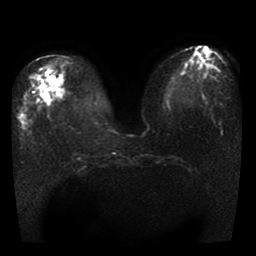
Breast MRI, one axial slice. Slice 14 of 41 in the series (ordered by position). Diffusion-weighted series; image 2 of 4 stored at this slice position (different b-values; order by instance number). 1.5 T. 5 mm slice thickness. 256 × 256 image matrix, field of view 330 × 330 mm. Female patient.
Annotated regions visible in this slice (expert manual segmentation):
- tumour on diffusion-weighted imaging: bounding box [x1, y1, x2, y2] px = [44, 91, 49, 99]